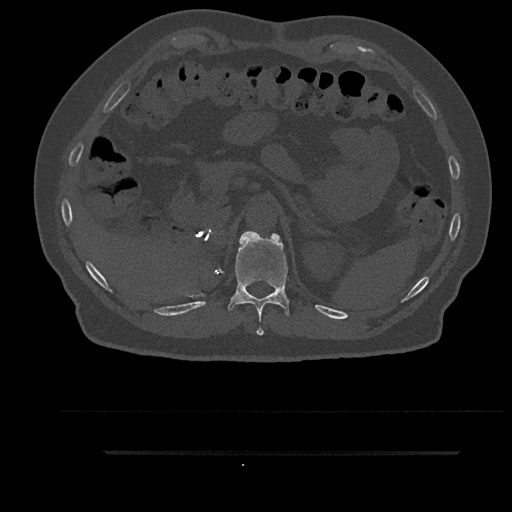
CT including the spine, one axial slice. Slice 300 of 797 in the series (ordered by position). Reconstruction kernel Br40s/3. Bone window (W 1800 / L 400 HU). 0.5 mm slice thickness. 512 × 512 image matrix. Male patient, age 63 years. From the clinical record (not read from this slice): primary cancer: renal; vertebrae with lytic lesions (as recorded): T8.
Structures marked on this image (semi-automatic segmentation, software-assisted and operator-edited):
- T11 vertebra: bounding box <221,231,293,336> (left, top, right, bottom; pixels)